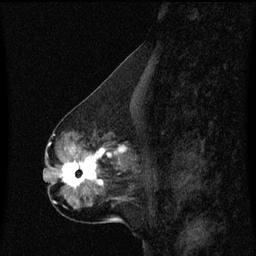
Breast MRI (dynamic contrast-enhanced), one sagittal slice; position 27 of 60 along the scan axis; dynamic contrast-enhanced series, image 2 of 3 at this slice position (ordered by acquisition); 1.5 T; TE 4.2 ms, TR 8.4 ms; 2 mm slice thickness; 256 × 256 image matrix, field of view 200 × 200 mm. Patient: female, 50 years. Case-level facts recorded for this patient, not image findings: setting: breast cancer imaged before/during neoadjuvant chemotherapy; receptor status: HR-positive, HER2-negative.
Outlined on this slice (semi-automatic segmentation, software-assisted and operator-edited):
- analysis volume of interest (the breast-tissue region the enhancement analysis was run in; not a lesion): bounding box <55,140,133,191> (left, top, right, bottom; pixels)
- tumour enhancement mask (voxels above the 70 % enhancement threshold inside the analysis volume of interest): <63,146,128,189>